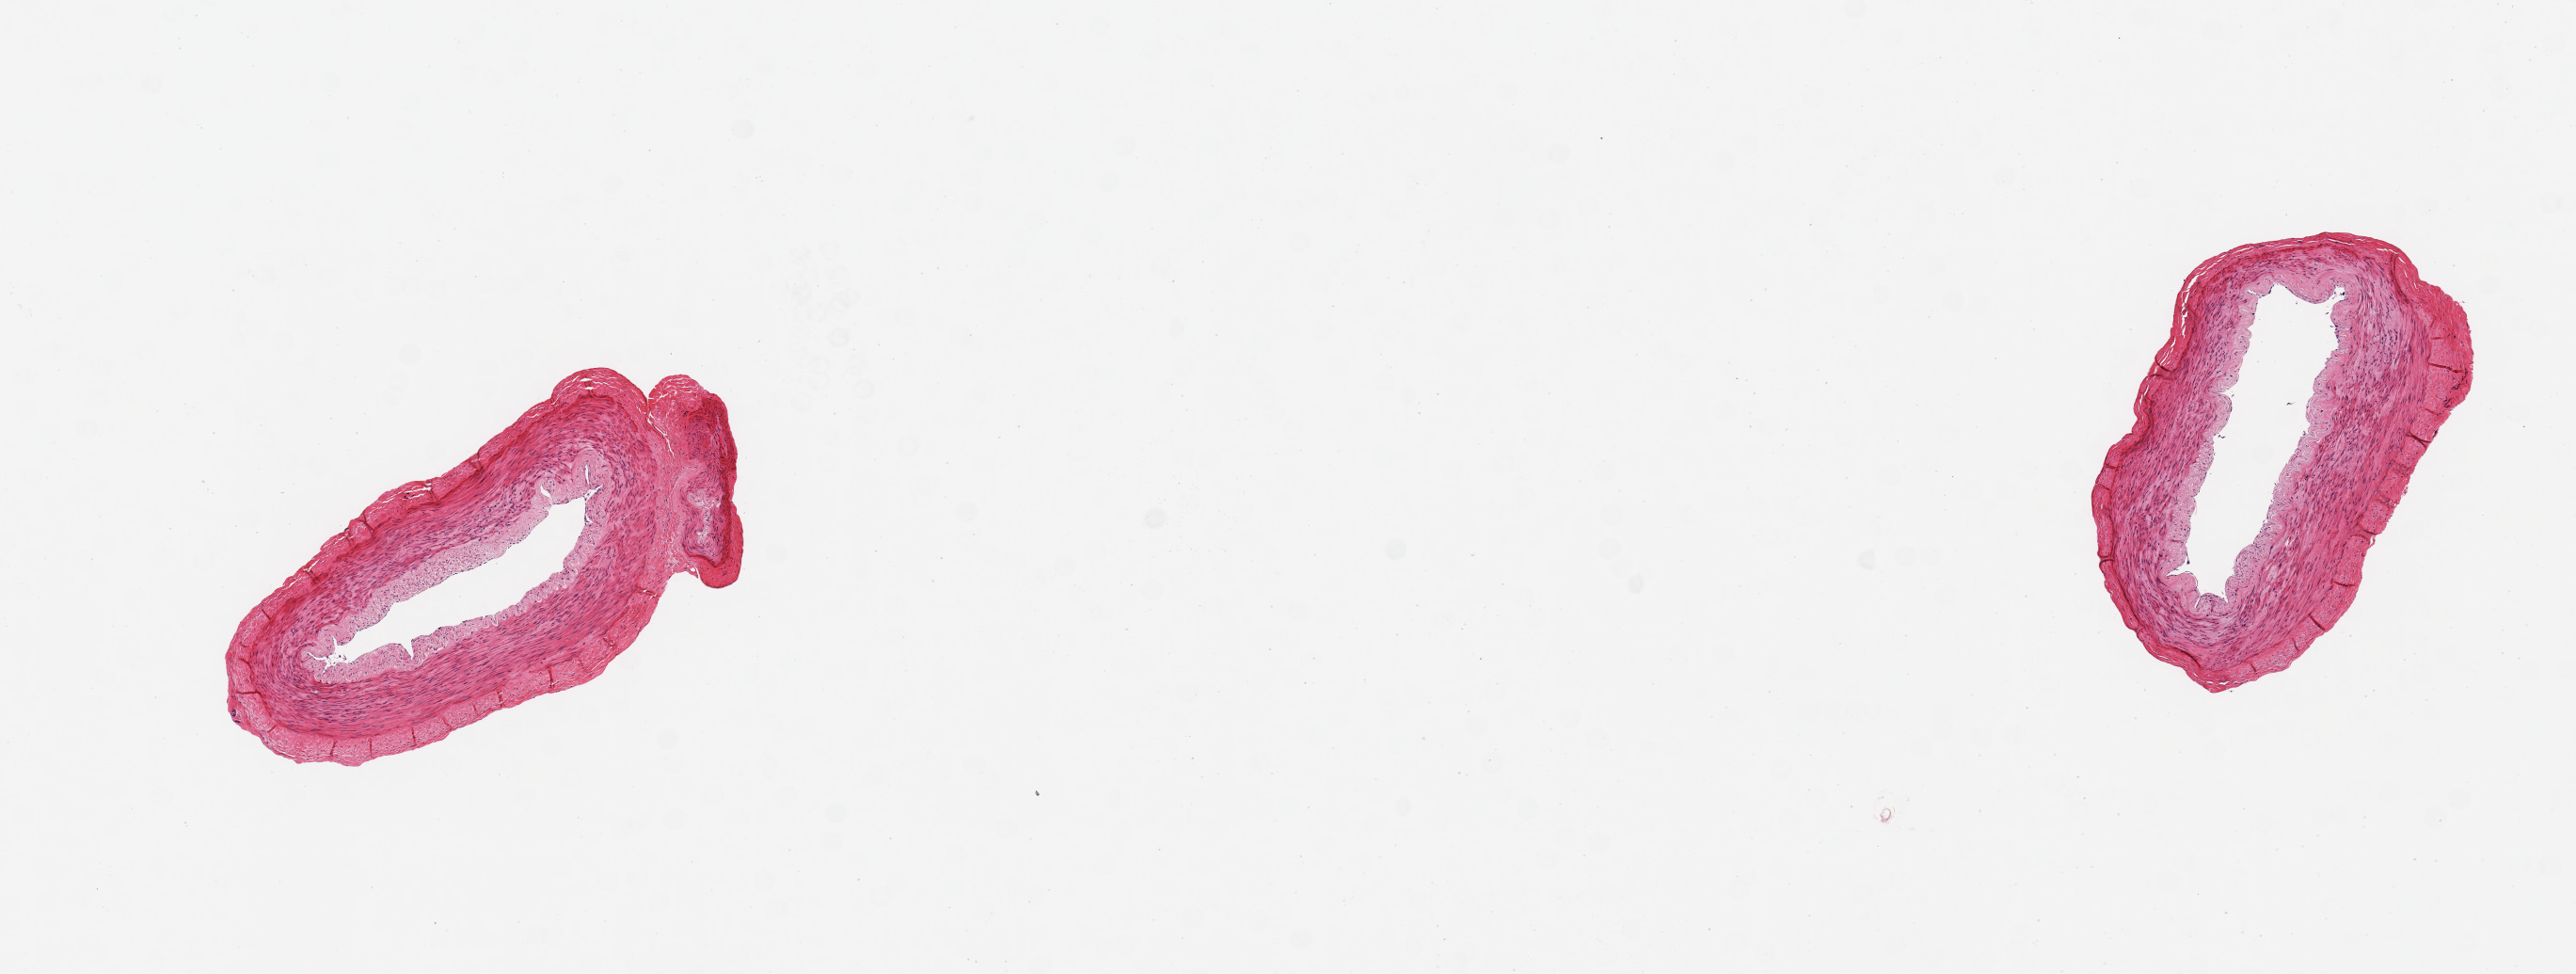
Digitized hematoxylin and eosin (H&E)-stained section, brightfield, low-resolution overview of the scanned area, about 10.8 x 4.1 mm (from a 20x scan); PAXgene-fixed, paraffin-embedded tissue; target tissue: tibial artery; donor tissue sample.
Reviewer comment on this tissue sample: 2 pieces, no significant atherosis or adherent fat.